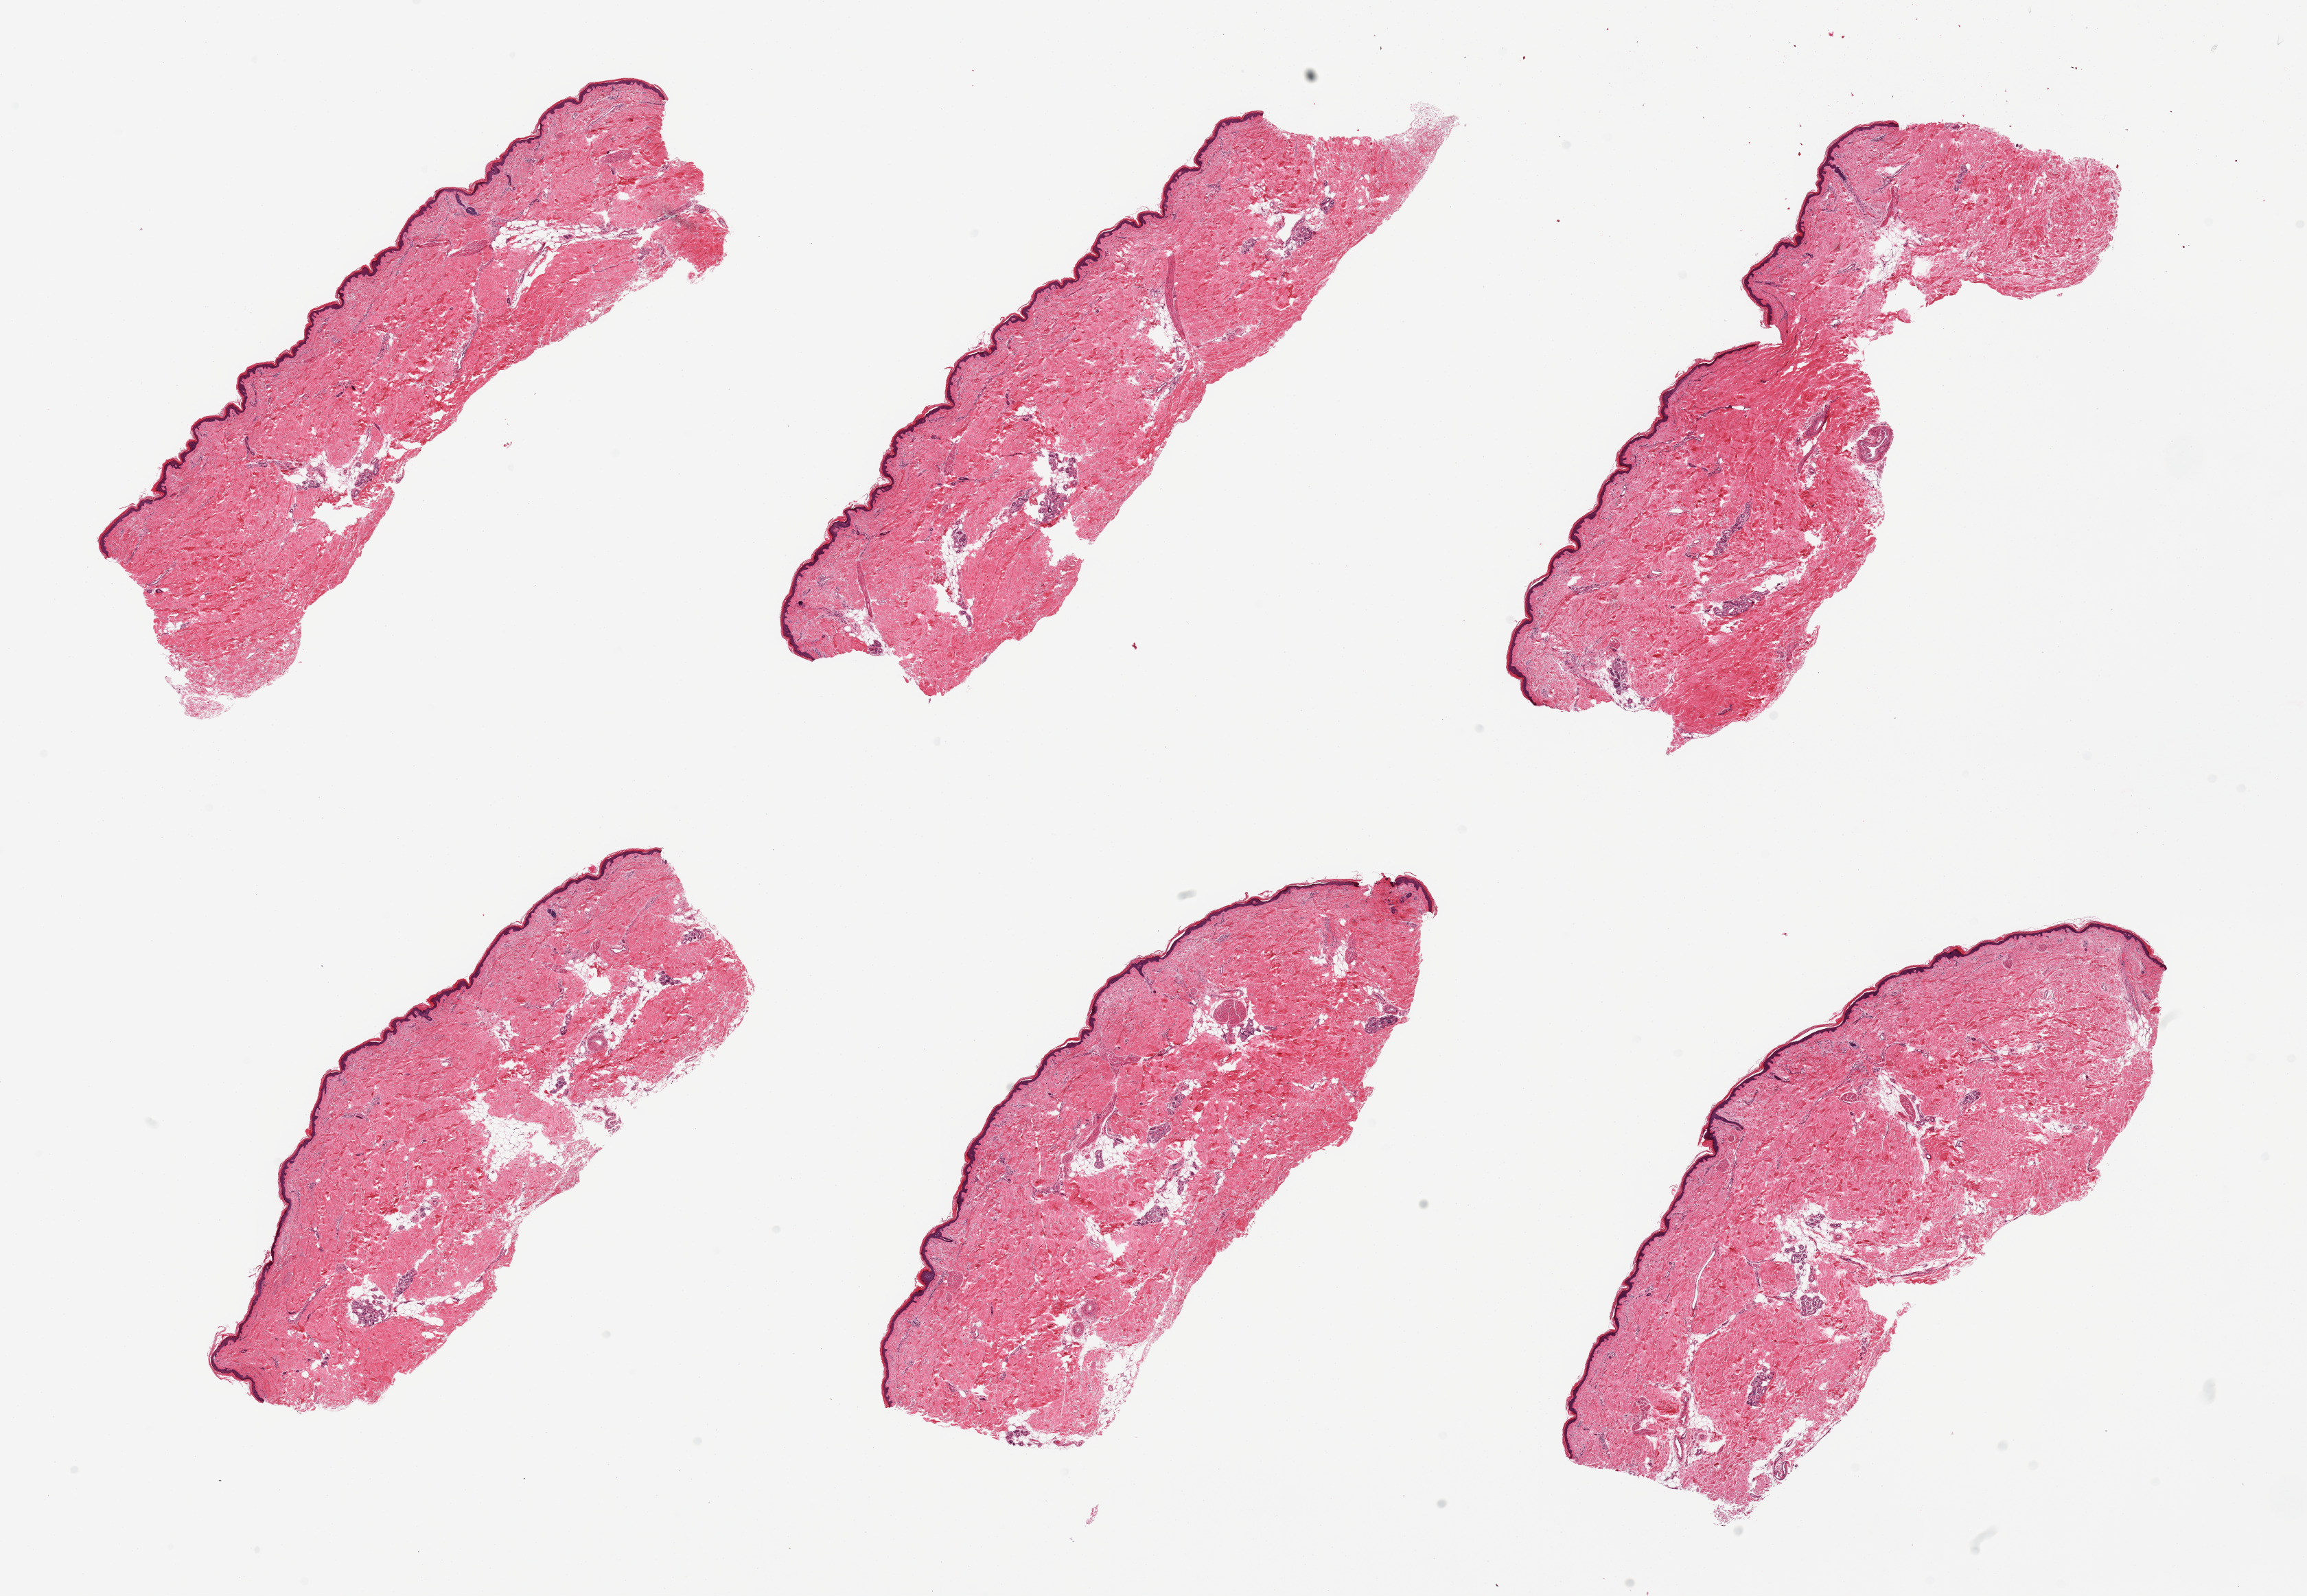
Digitized hematoxylin and eosin (H&E)-stained section — shown as a low-resolution overview of the whole scanned area (about 26.6 x 18.4 mm, slide scanned at 20x); PAXgene-fixed, paraffin-embedded tissue; sampled site (target tissue): skin of lower leg; donor tissue sample. Donor sex: male.
Reviewer comment on this tissue sample: 6 pieces; ~10% internal fat (periadnexal); well trimmed.